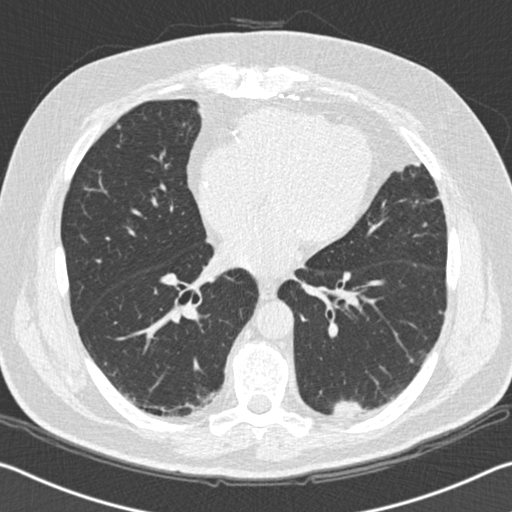
Low-dose screening chest CT, one axial slice; slice 80 of 172 in the series (ordered by position); 120 kVp; lung window (W 1500 / L -600 HU); 512 × 512 image matrix, field of view 340 × 340 mm.
Annotated regions visible in this slice (outlined manually by an expert reader):
- lesion 1 (tumor, lower lobe of left lung): bounding box (x1, y1, x2, y2) in pixels: (332, 400, 367, 418)